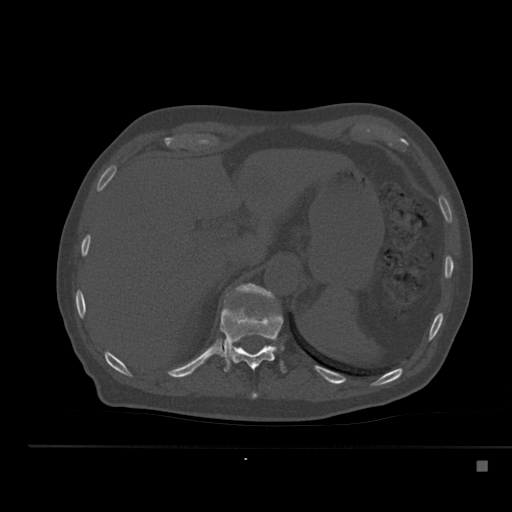
CT including the spine, one axial slice; slice 247 of 517 in the series (ordered by position); reconstruction kernel Br40s; 120 kVp; bone window (W 1800 / L 400 HU); 1.5 mm slice thickness; 512 × 512 image matrix, field of view 408 × 408 mm. Patient: male, 70 years. From the clinical record (not read from this slice): primary cancer: renal; vertebrae with lytic lesions (as recorded): T4, T6, T10, T12, L3, L4, L5.
Outlined on this slice (semi-automatically segmented with operator editing):
- T10 vertebra: bounding box [x1, y1, x2, y2] px = [252, 394, 257, 398]
- T11 vertebra: [220, 304, 287, 398]
- T12 vertebra: [227, 283, 277, 354]